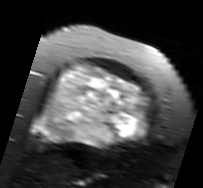
MRI of an extremity soft-tissue mass, one axial slice; slice 53 of 91 in the series (ordered by position); T2-weighted fat-saturated; MR volume resampled by the dataset authors to the PET/CT grid (not the native acquisition matrix); 203 × 188 image matrix, field of view 198 × 184 mm. Female patient. From the clinical record (not read from this slice): histological type: malignant solitary fibrous tumor; grade: intermediate; site of the primary tumour: right thigh.
Outlined on this slice (expert contour drawn on MRI and transferred to this co-registered scan by the dataset authors):
- gross tumour volume including surrounding oedema: box from (x=31, y=63) to (x=153, y=148) px
- gross tumour volume (mass): (x=33, y=65)–(x=148, y=148)